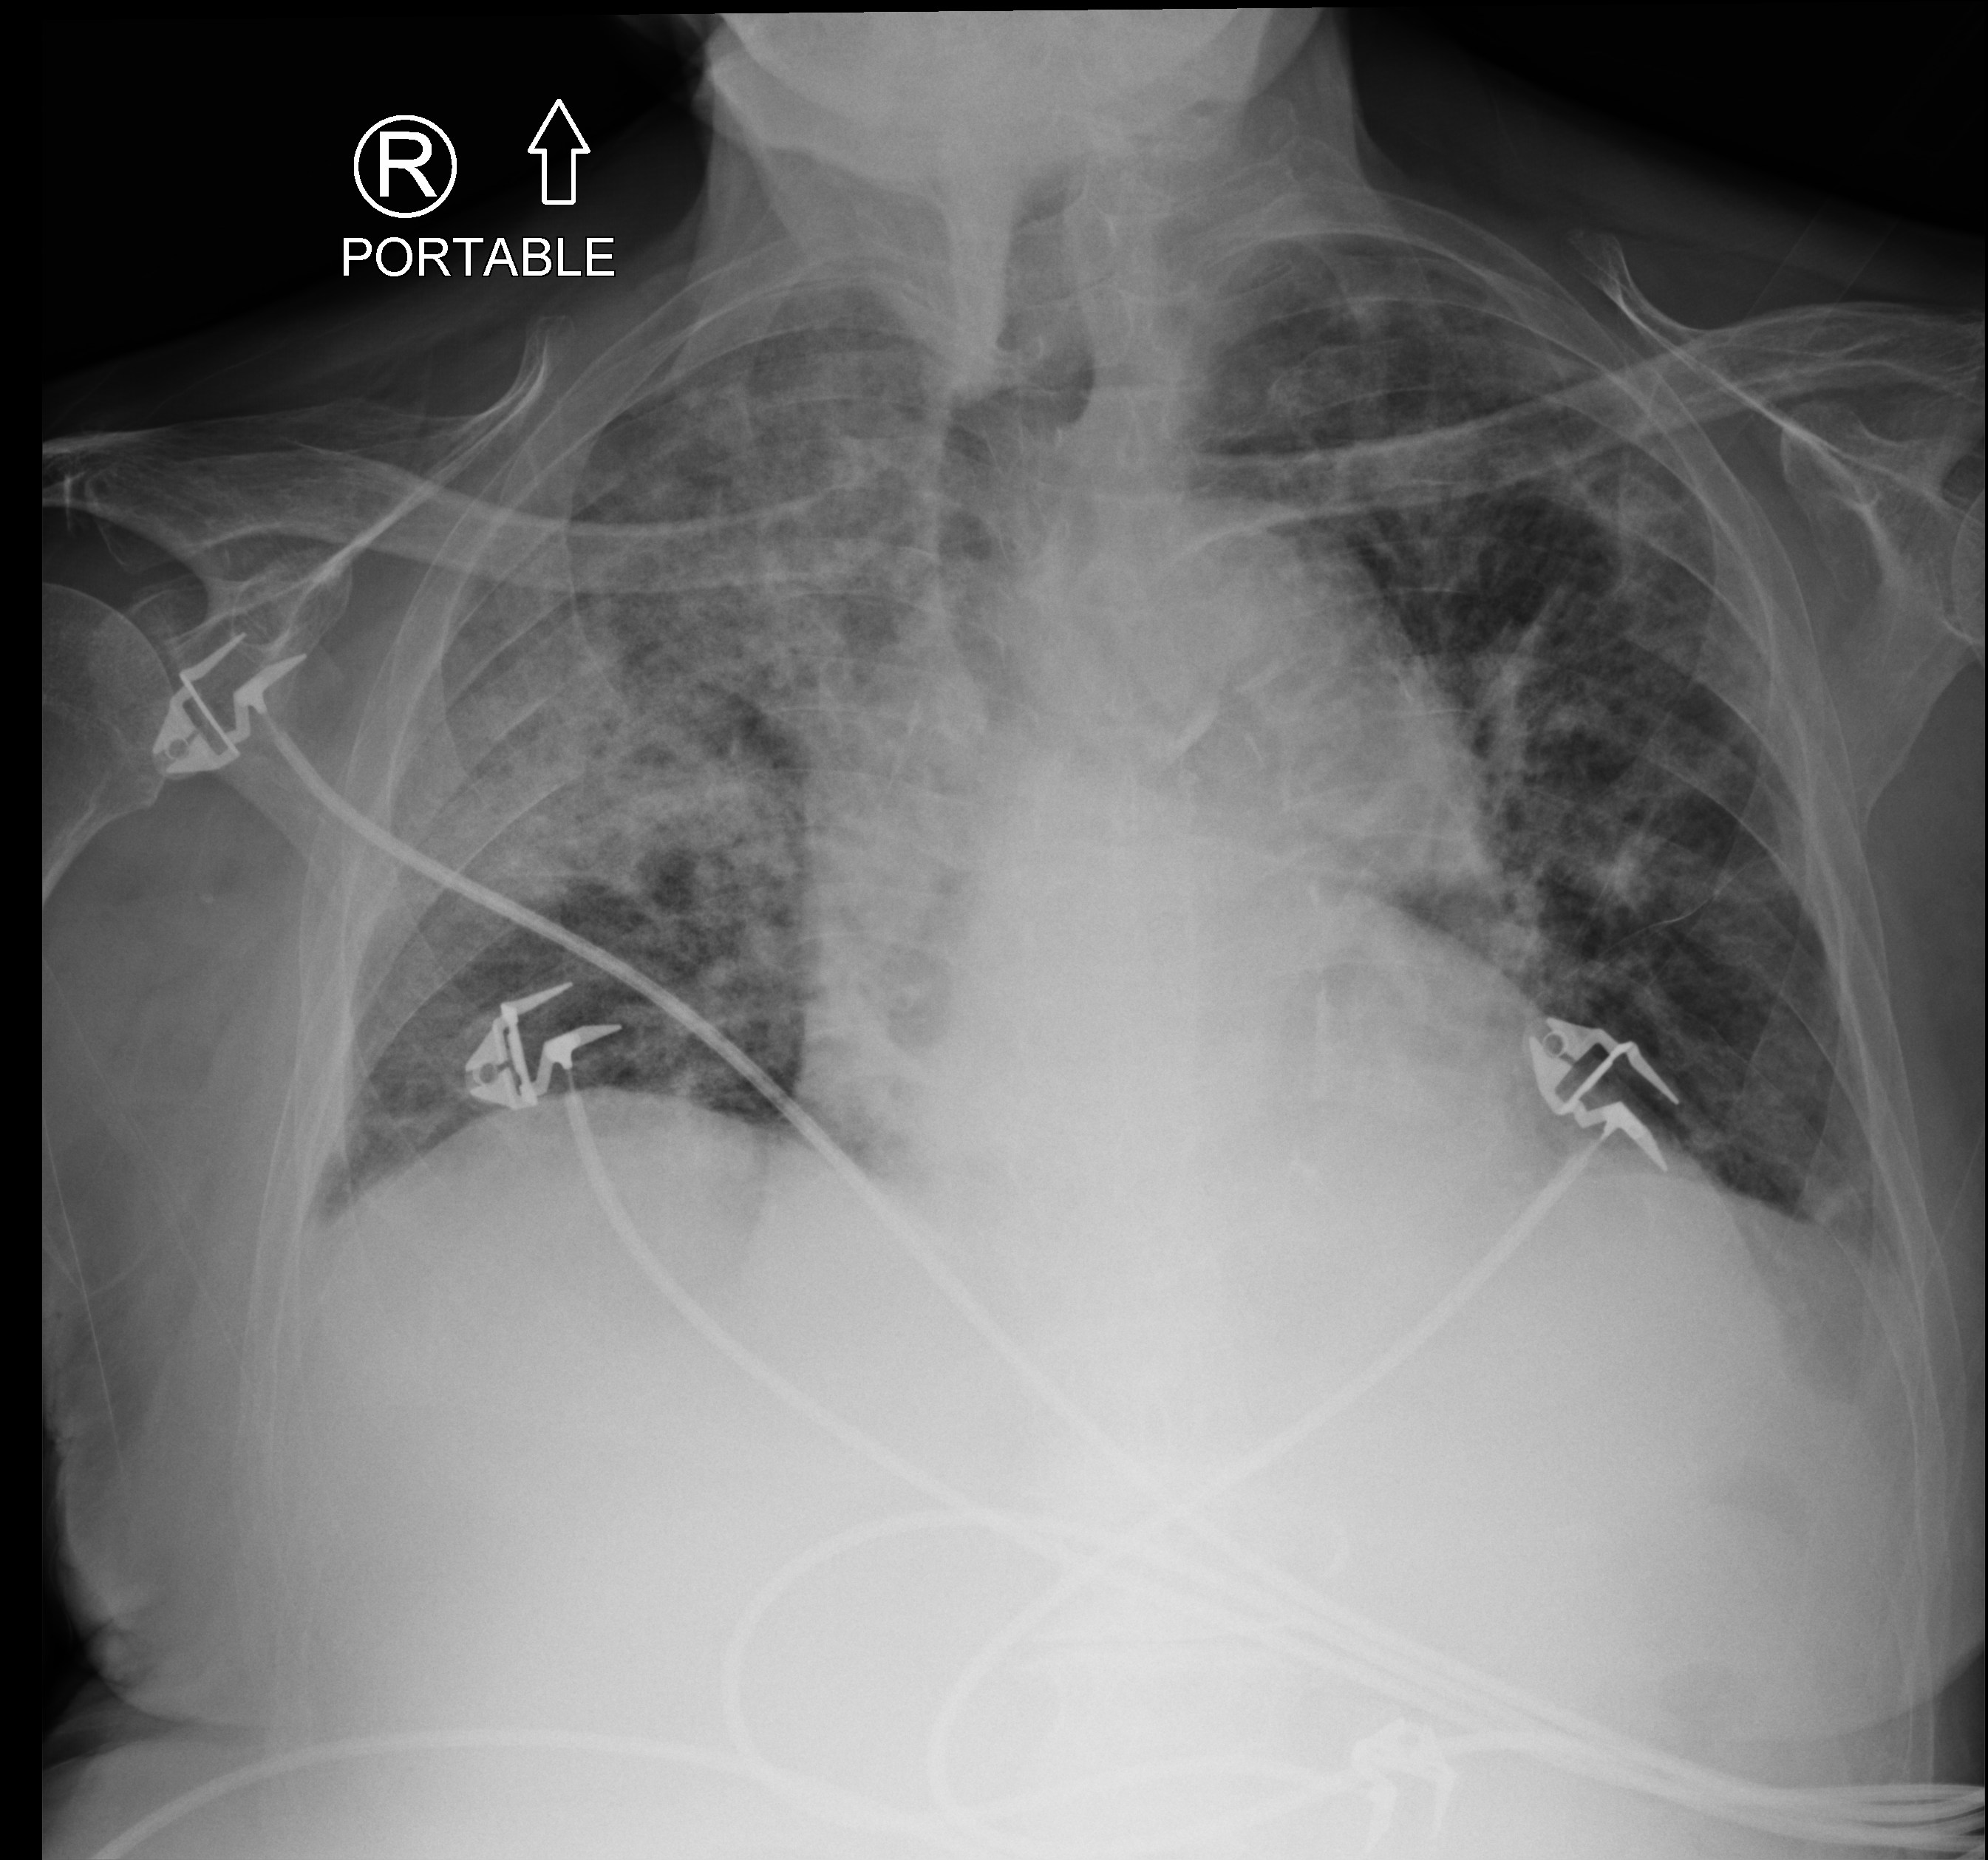
Bedside chest radiograph (computed radiography); anteroposterior (AP) projection. Male patient hospitalised with COVID-19, age 75–90 years.
Admission-level facts for this patient (not findings on this image; timing relative to this image not recorded):
- chronic kidney disease (admission record): yes
- other chronic lung disease (admission record): no
- mechanically ventilated during this hospital stay: no